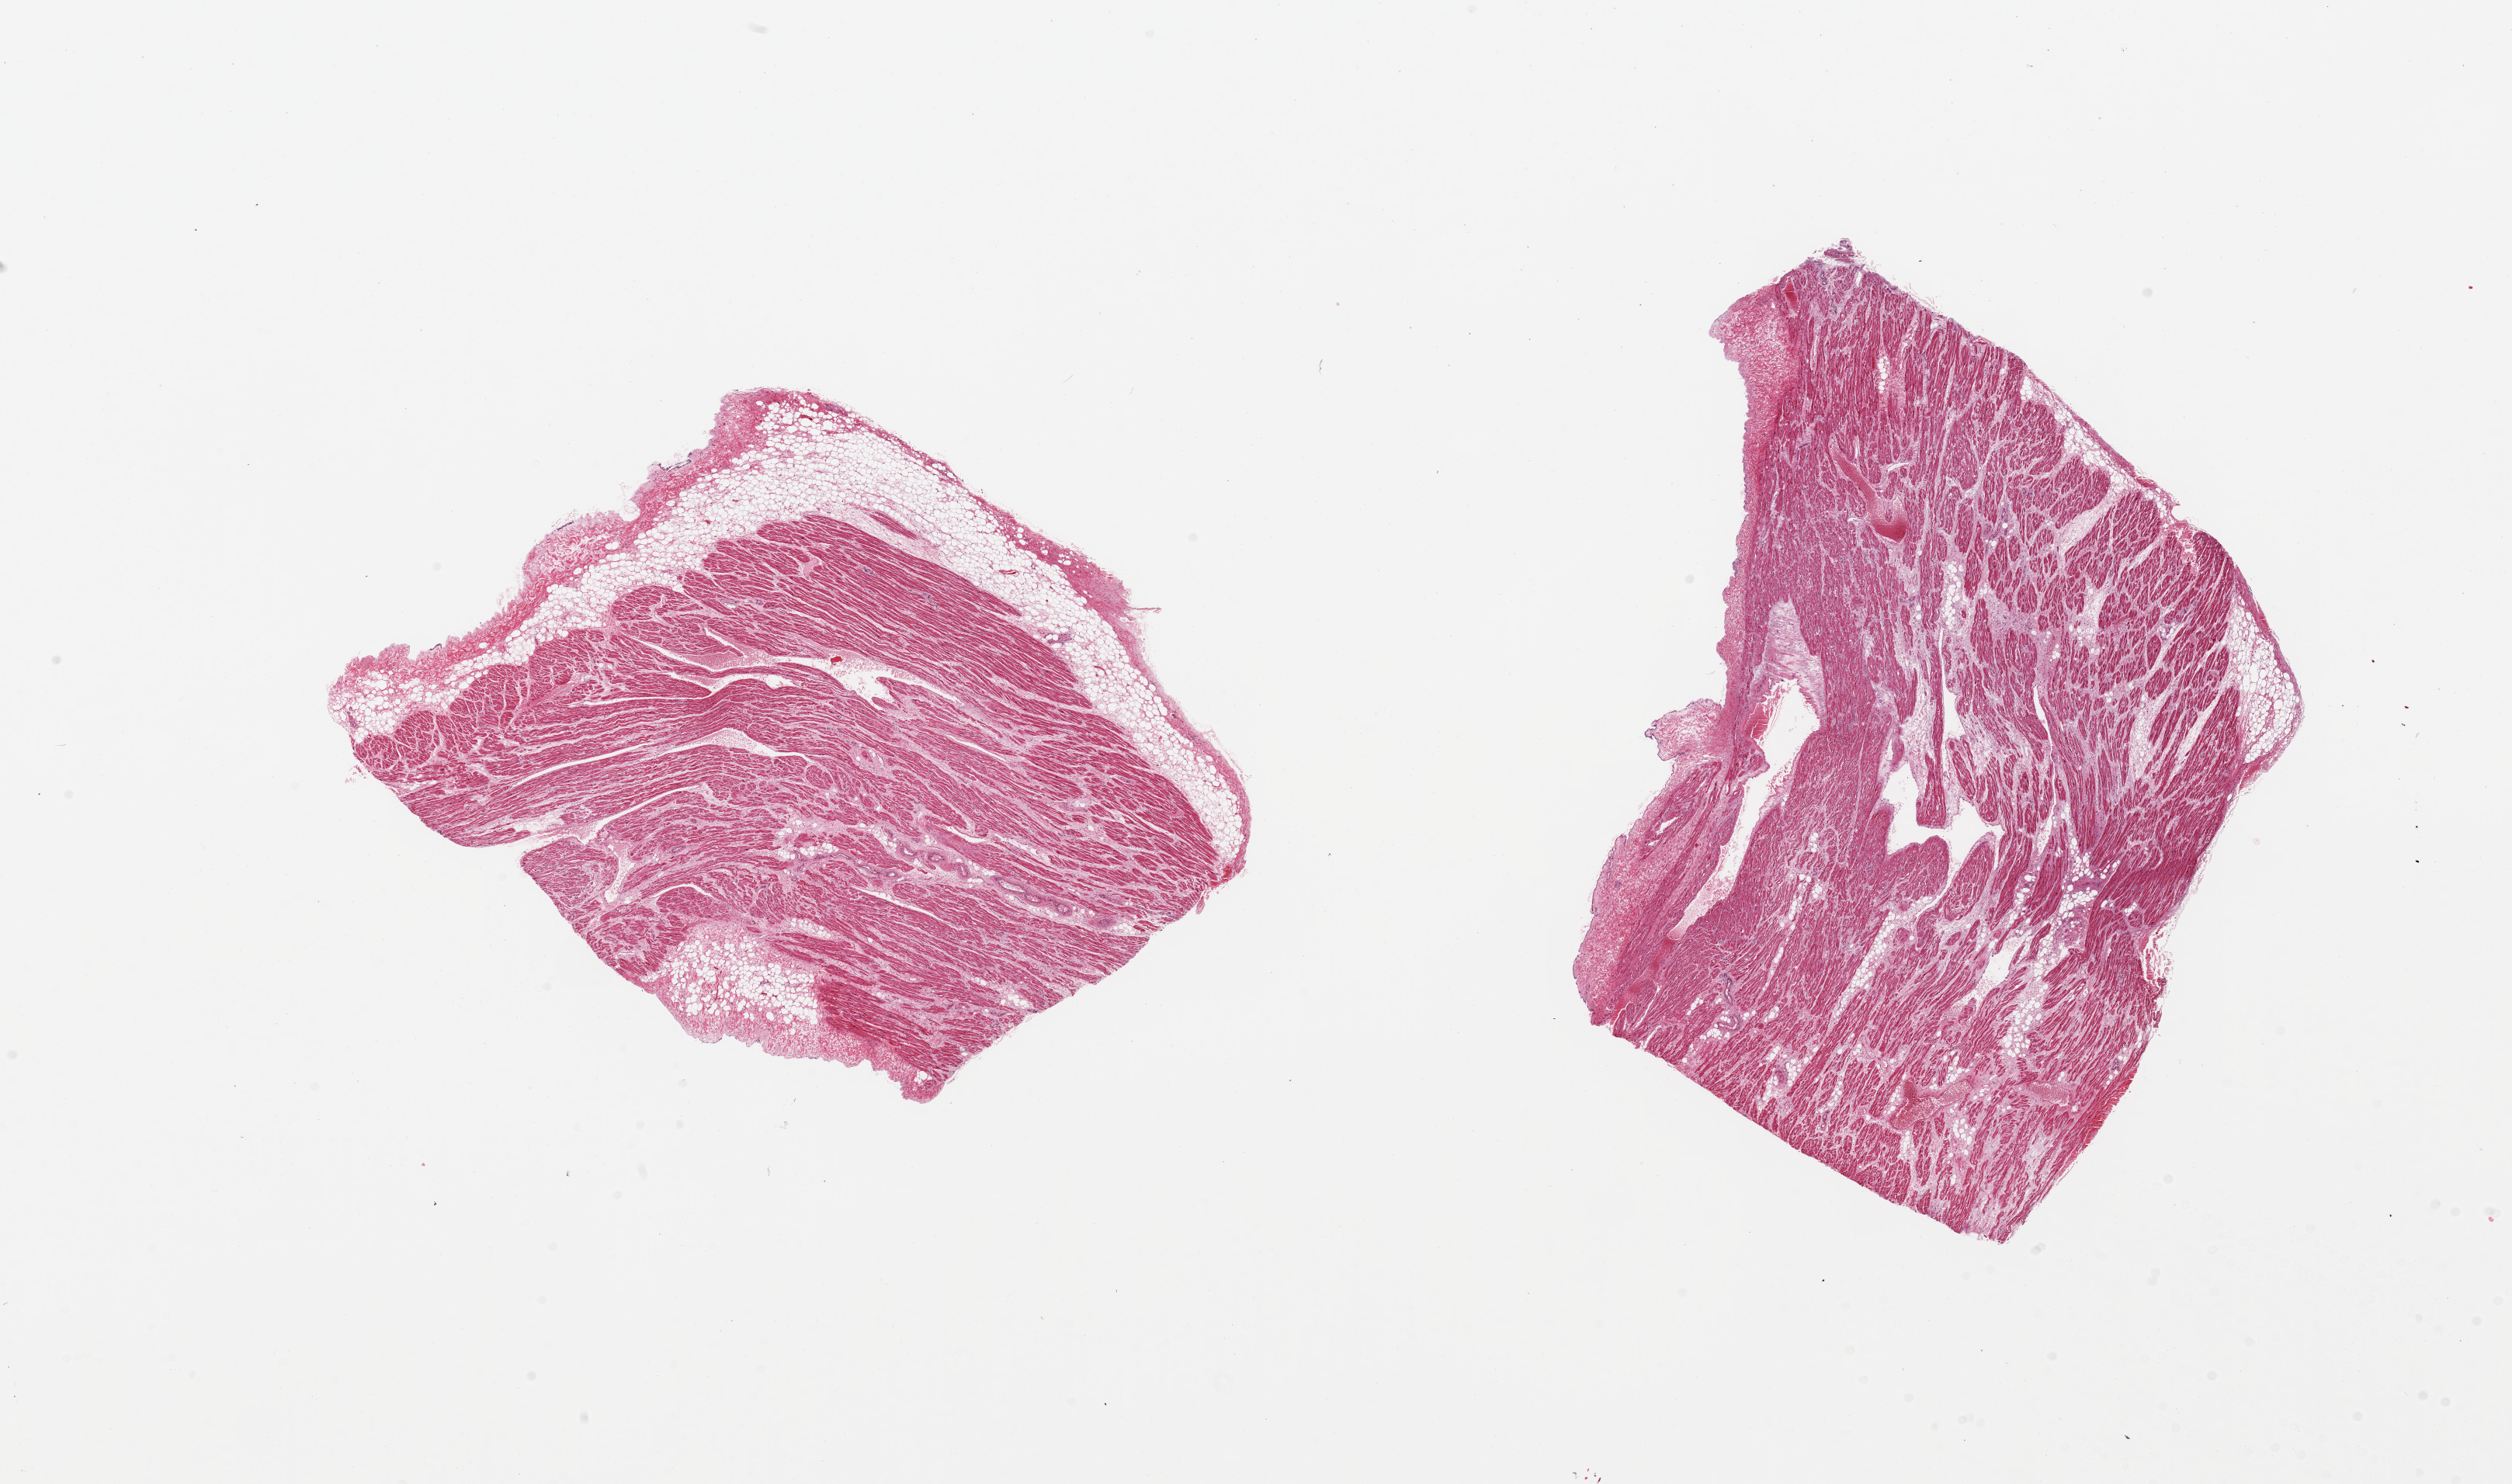
Whole-slide image, H&E stain, brightfield, whole scanned area (about 25.6 x 15.1 mm, acquisition: 20x scan) shown as a low-resolution overview. PAXgene-fixed, paraffin-embedded tissue. Target tissue: auricular appendage. Tissue donor sample. Male donor.
Review note (as recorded): 2 pieces; 20% & 5% external fat.